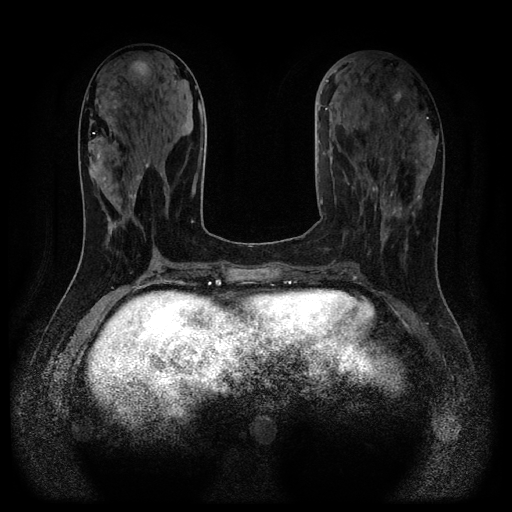
Breast MRI (dynamic contrast-enhanced, multi-phase), one axial slice. Position 44 of 116 along the scan axis. Dynamic contrast-enhanced series, time point 2 of 5 at this slice position (early post-contrast). 1.5 T. TE 2.7 ms, TR 5.4 ms. 2.2 mm slice thickness. 512 × 512 image matrix, field of view 330 × 330 mm. Female patient, age 43 years.
Structures marked on this image (semi-automatically segmented with operator editing):
- breast lesion (labelled benign in the annotation): box from (x=128, y=58) to (x=151, y=83) px